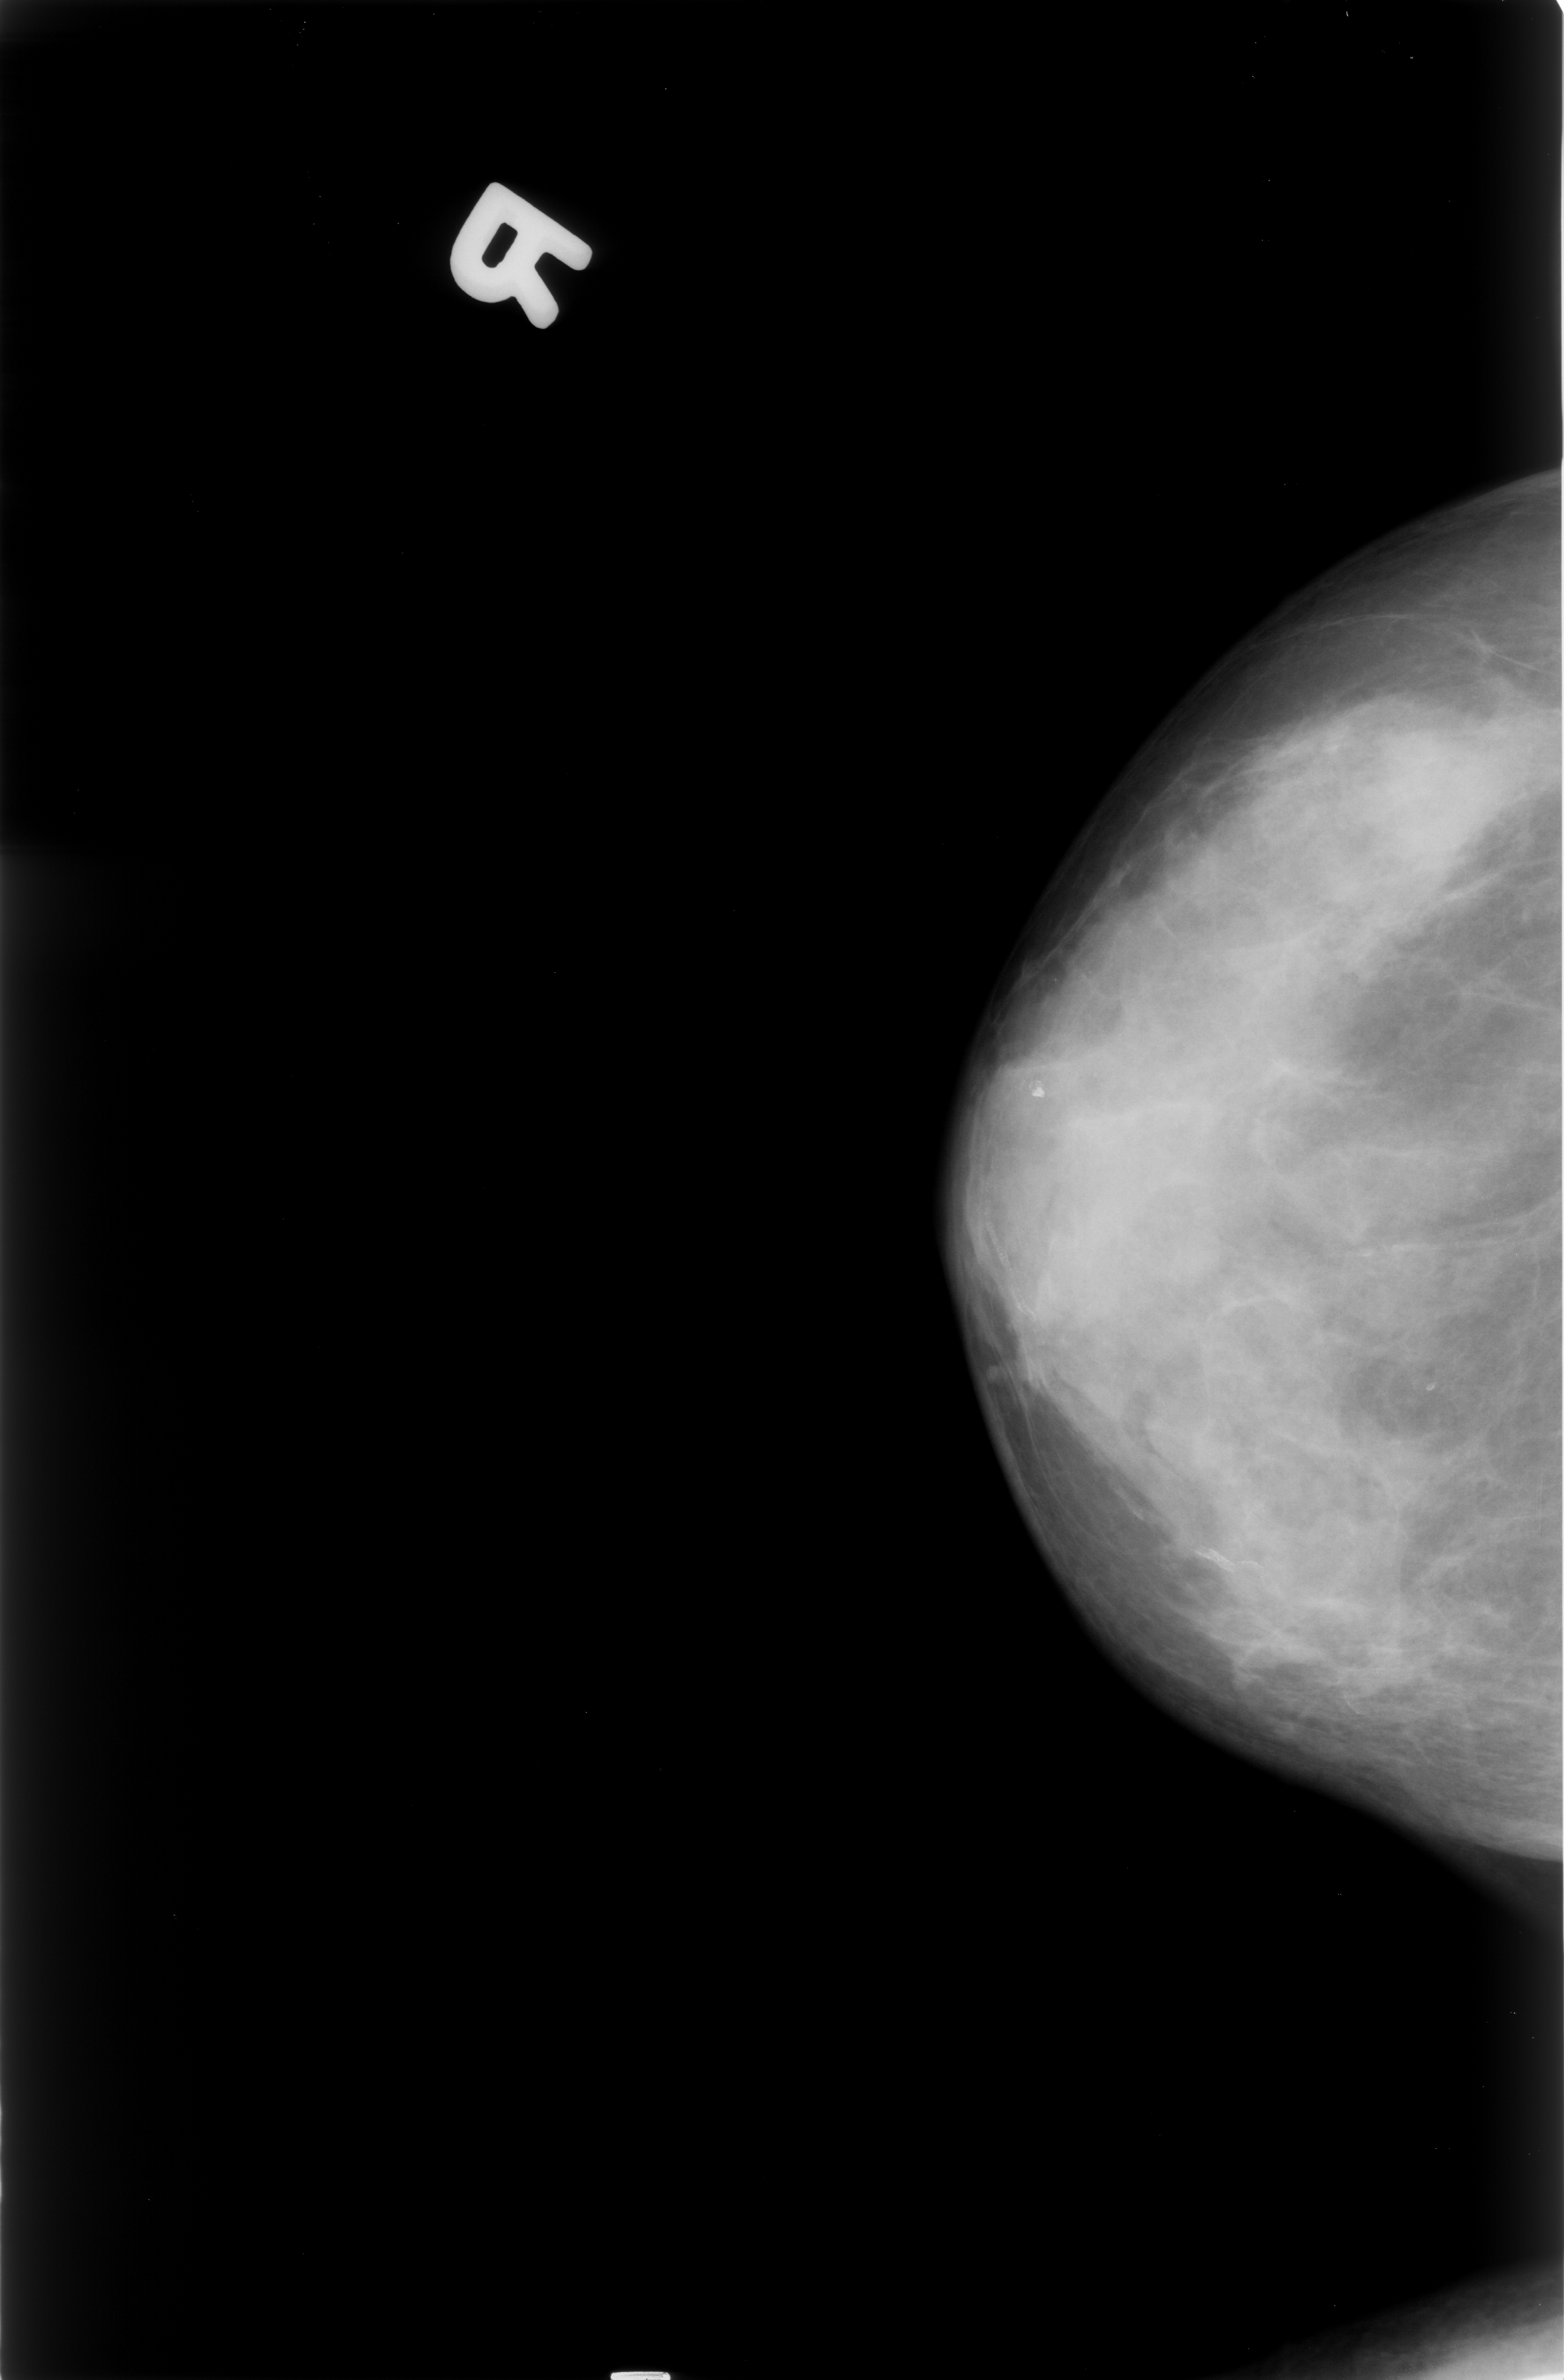
Scanned film-screen mammogram; right breast; craniocaudal (CC) view; BI-RADS breast density category 4 (scale 1–4).
Marked findings (only marked abnormalities are described; nothing is implied about the rest of the image): mass, shape irregular, margins obscured; BI-RADS assessment category 4; subtlety rating 3 on a 1 (subtle) to 5 (obvious) scale; pathology result (as recorded, not read from the image): malignant.